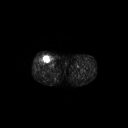
FDG PET of an extremity soft-tissue mass (from a PET/CT study), one axial slice. Slice 268 of 311 in the series (ordered by position). 3.27 mm slice thickness. 128 × 128 image matrix, field of view 700 × 700 mm. Male patient, age 56 years. From the clinical record (not read from this slice): histological type: pleiomorphic leiomyosarcoma; grade: intermediate; site of the primary tumour: right thigh.
Outlined on this slice (expert contour drawn on MRI and transferred to this co-registered scan by the dataset authors):
- gross tumour volume including surrounding oedema: box from (x=40, y=54) to (x=51, y=63) px
- gross tumour volume (mass): (x=41, y=55)–(x=51, y=63)